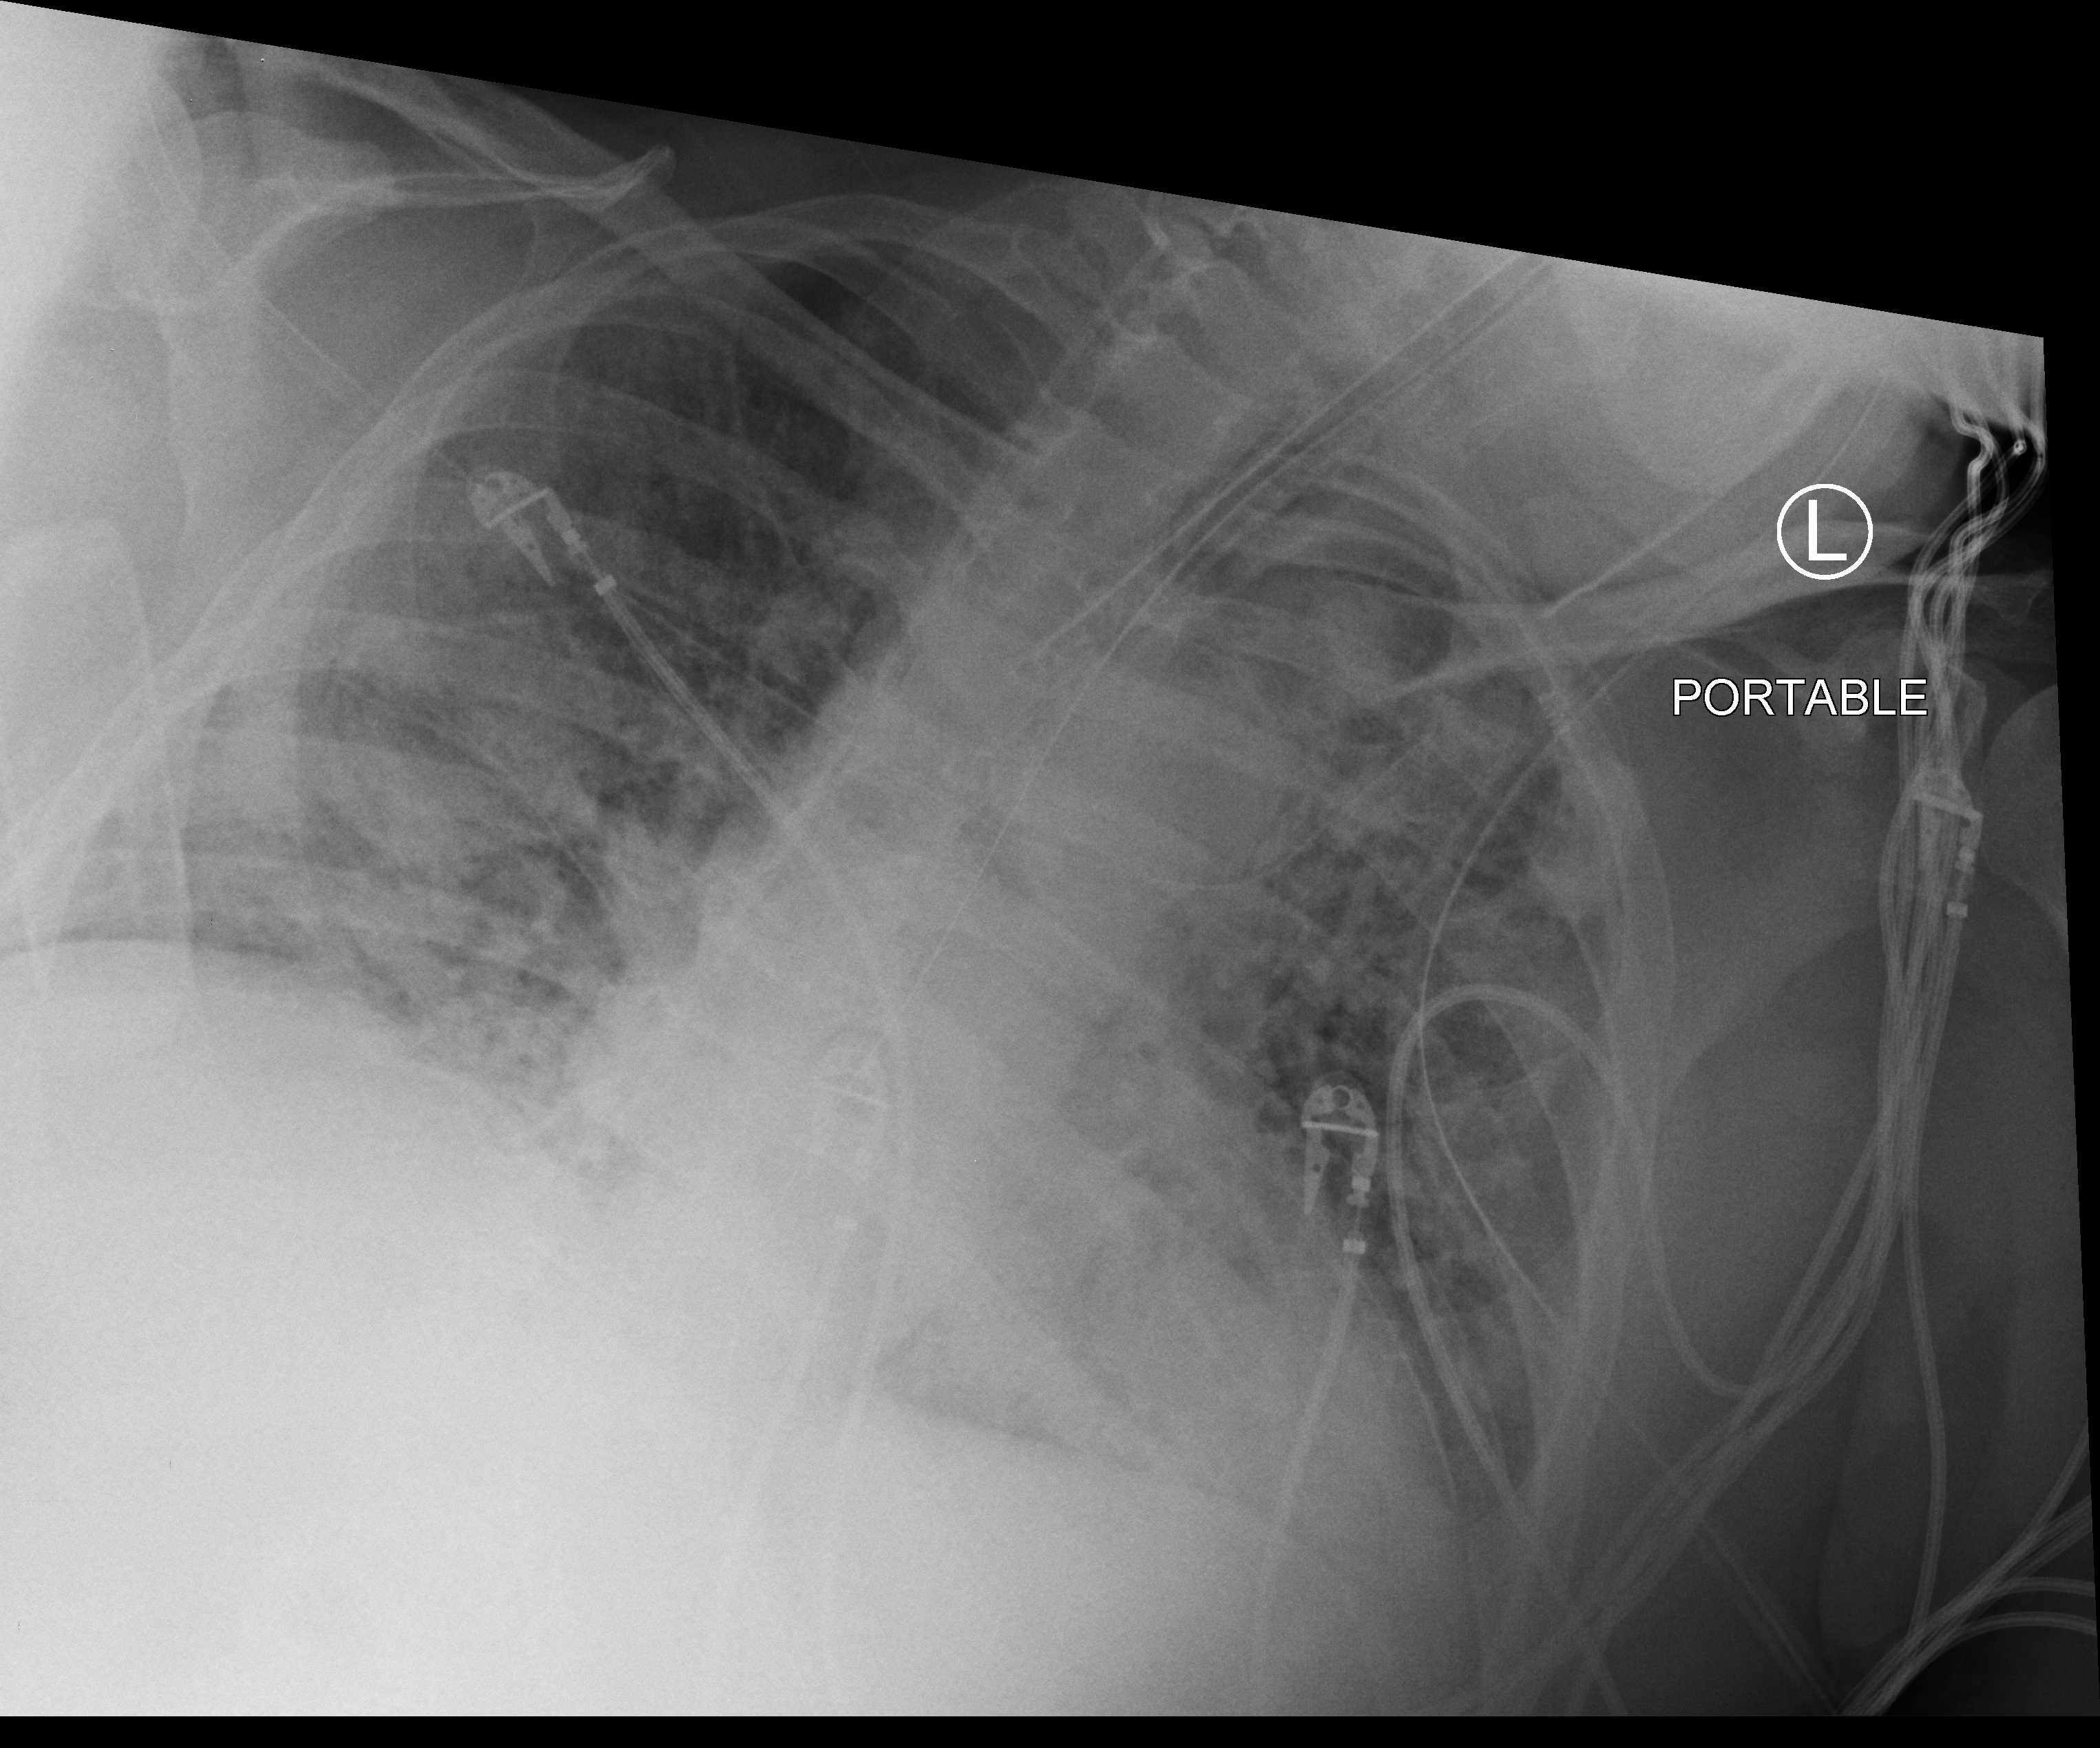
Chest X-ray (portable), anteroposterior (AP) projection. Male patient hospitalised with COVID-19, age 60–74 years.
From the hospital-stay record, not from the radiograph (when in the stay this image was taken is not recorded):
- smoking status (admission record): never